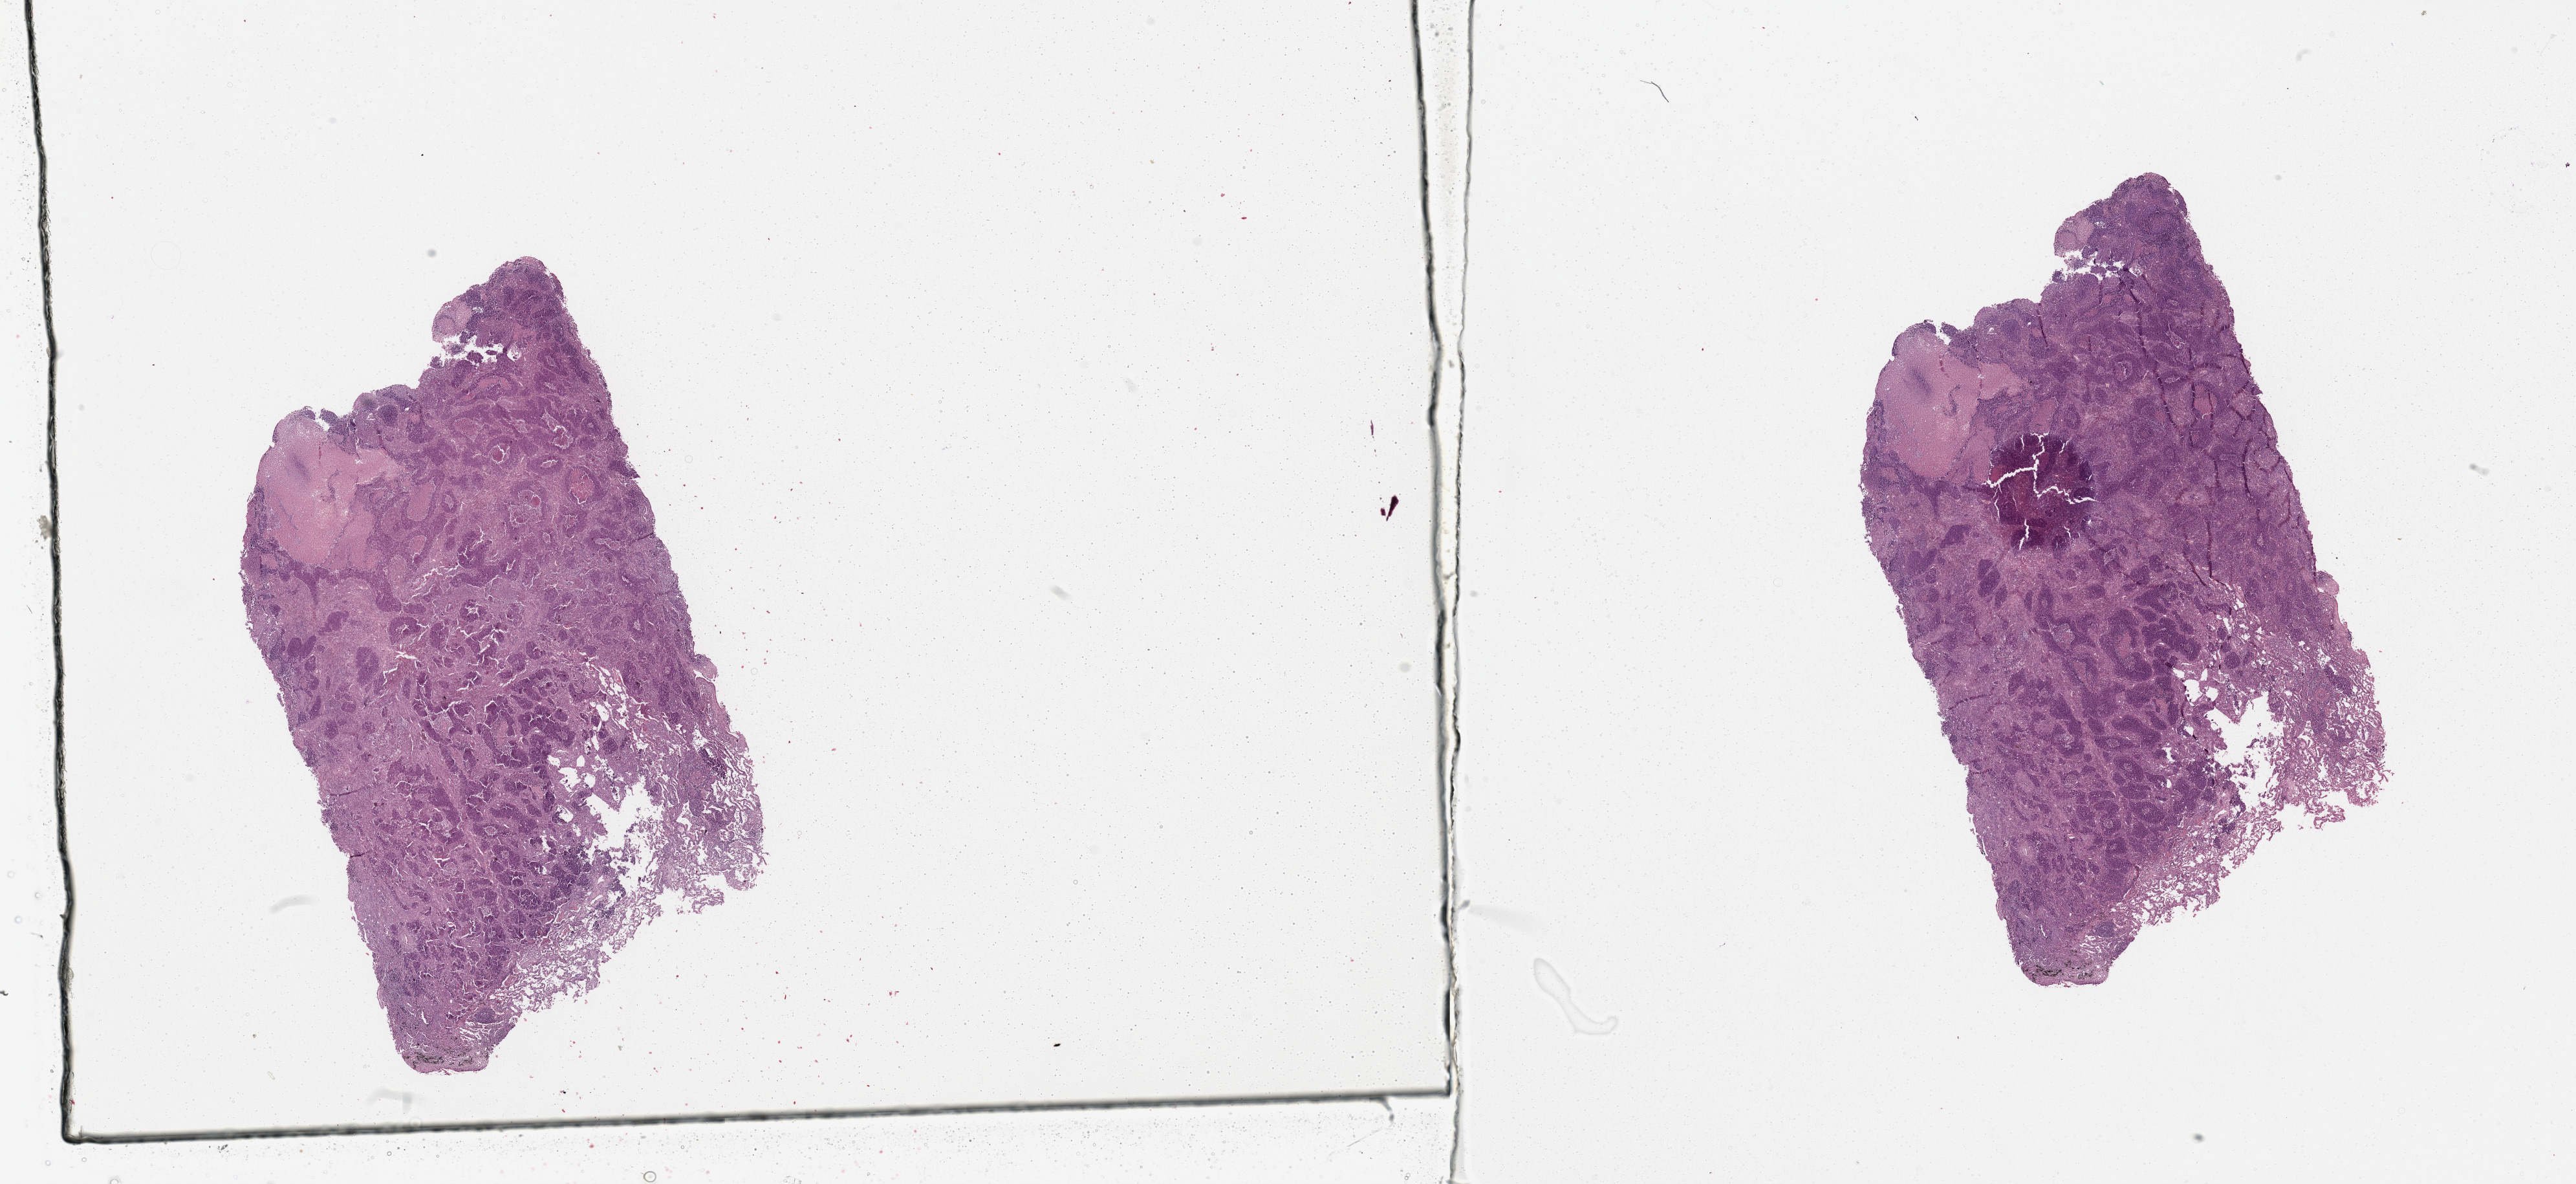
Whole-slide histology image, H&E, whole scanned area (about 31.5 x 14.5 mm) shown as a low-resolution overview, lung, tumour tissue. Male, 60 y/o.
Diagnosis: Squamous cell carcinoma, NOS.